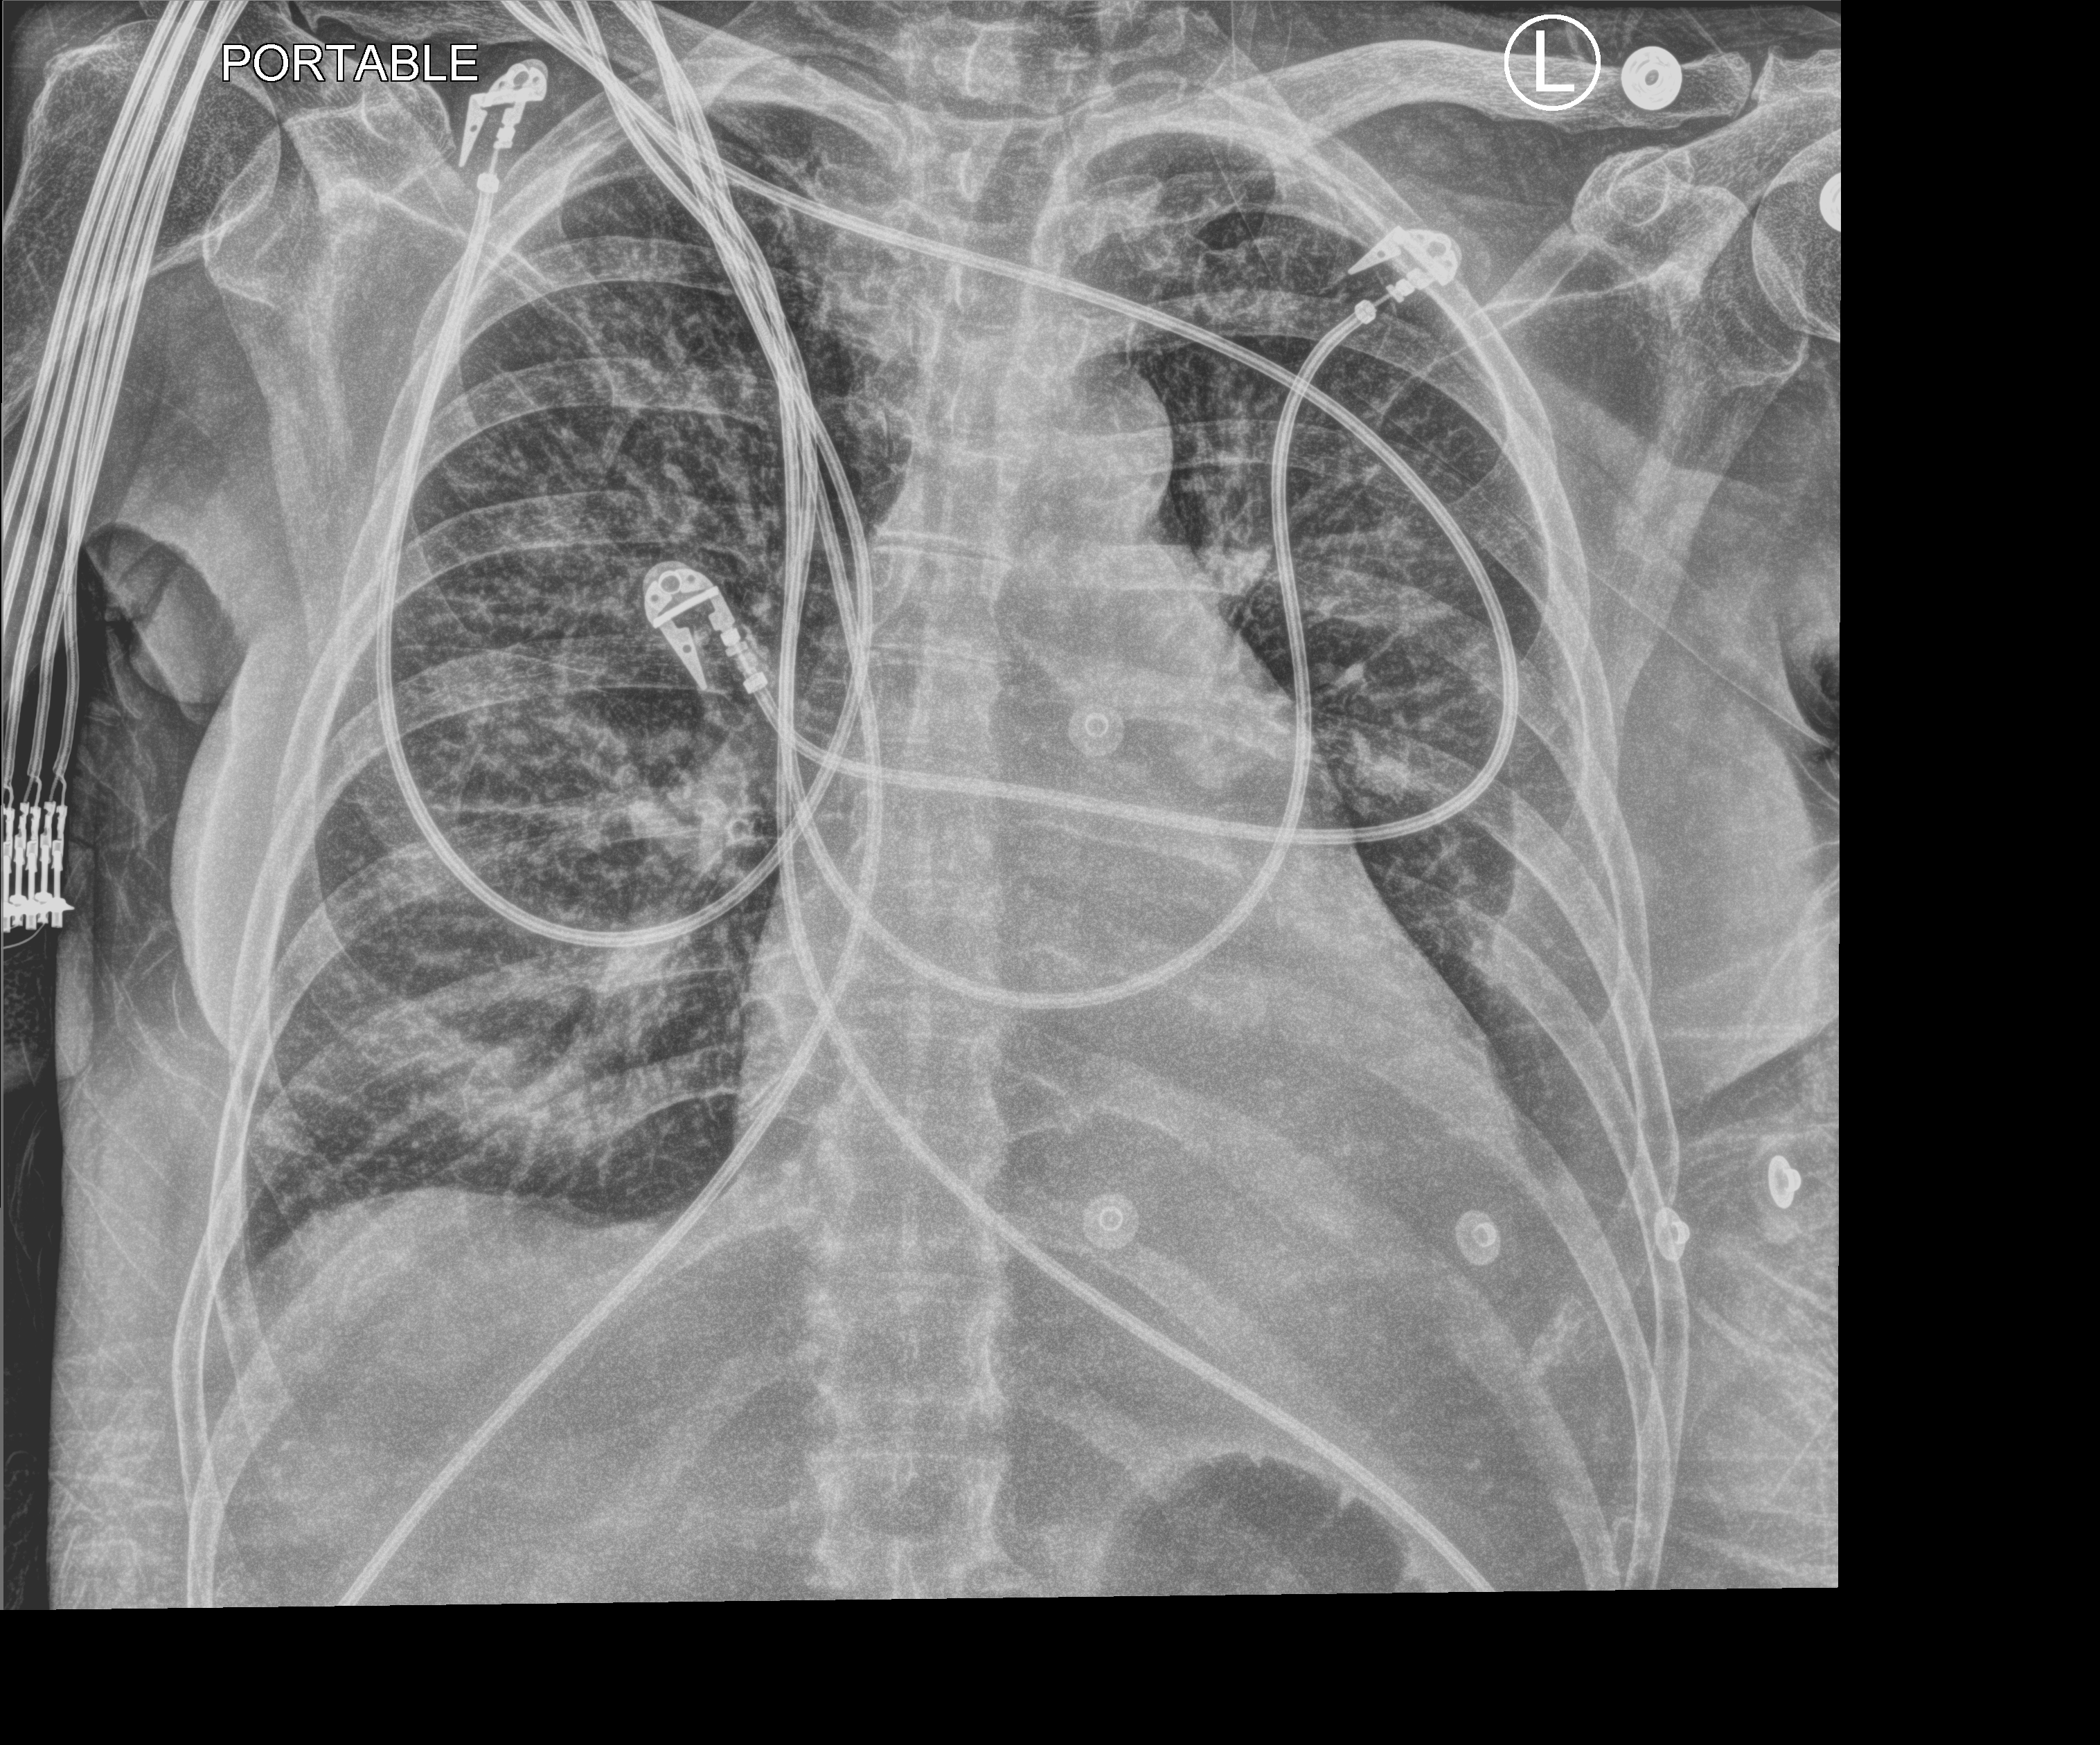
Portable chest radiograph, anteroposterior (AP) projection. Female patient hospitalised with COVID-19, age 60–74 years.
From the hospital-stay record, not from the radiograph (when in the stay this image was taken is not recorded):
- mechanically ventilated during this hospital stay: yes